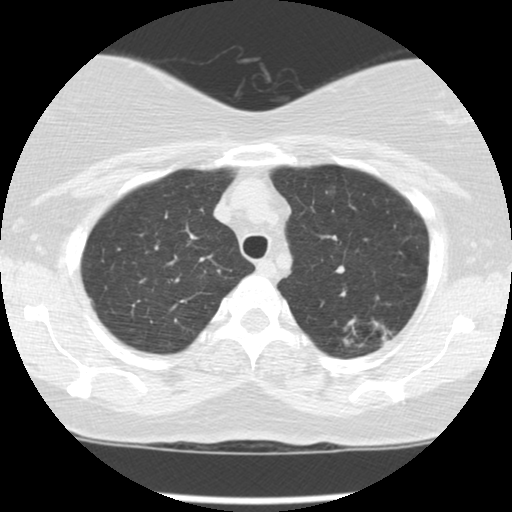
Low-dose screening chest CT, one axial slice. Slice 106 of 127 in the series (ordered by position). Reconstruction kernel STANDARD. 120 kVp. Lung window (W 1500 / L -600 HU). 2.5 mm slice thickness. 512 × 512 image matrix.
Structures marked on this image (manually delineated by an expert):
- lesion 1 (tumor, upper lobe of left lung): bounding box (x1, y1, x2, y2) in pixels: (373, 319, 393, 347)